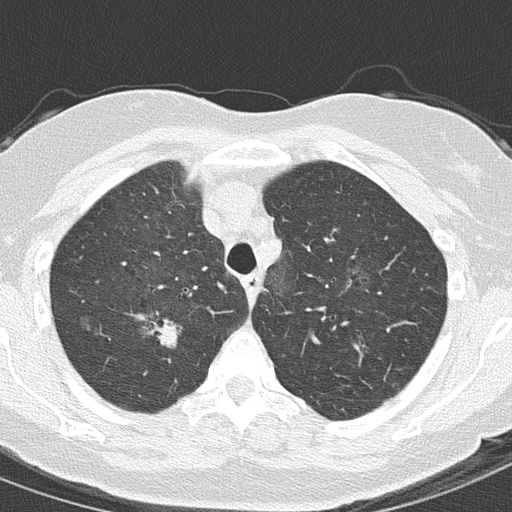
Chest CT (low-dose screening protocol), one axial image; second screening round (one year after baseline); lung window (W 1500 / L -600 HU); 2 mm slice thickness; lung (sharp) reconstruction kernel (B50f); 120 kVp; 512 × 512 image matrix, field of view 280 × 280 mm. Female, age 61 years at enrolment.
- Expert-annotated lung lesion, bounding box (x1, y1, x2, y2) in pixels: (145, 309, 187, 348).
- Screening reader's record for this exam (one nodule recorded; not confirmed to be the boxed lesion): non-calcified nodule or mass ≥4 mm, right upper lobe, 15 × 10 mm, spiculated (stellate) margins, ground glass attenuation, pre-existing on the prior screen: yes; interval growth: yes.
- Official screen result: positive, other.
- Lung cancer was diagnosed 91 days after this screen: adenocarcinoma, NOS, right upper lobe, moderately differentiated (G2), stage IA (AJCC 6th edition), 20 mm at pathology.